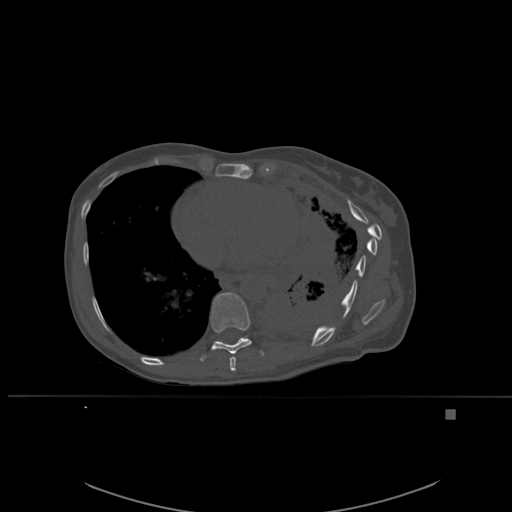
CT including the spine, one axial slice. Position 333 of 537 along the scan axis. Bone window (W 1800 / L 400 HU). 512 × 512 image matrix, field of view 440 × 440 mm. Patient: female, 45 years. From the clinical record (not read from this slice): primary cancer: lung.
Outlined on this slice (semi-automatically segmented with operator editing):
- T8 vertebra: box from (x=229, y=357) to (x=236, y=372) px
- T9 vertebra: (x=200, y=293)–(x=264, y=362)